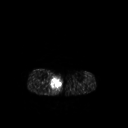
FDG PET of an extremity soft-tissue mass (from a PET/CT study), one axial slice; slice 129 of 267 in the series (ordered by position); 3.27 mm slice thickness; 128 × 128 image matrix, field of view 500 × 500 mm. Patient: male, 69 years. Case-level facts recorded for this patient, not image findings: histological type: pleiomorphic liposarcoma; grade: high; site of the primary tumour: right calf.
Outlined on this slice (expert contour drawn on MRI and transferred to this co-registered scan by the dataset authors):
- gross tumour volume including surrounding oedema: bounding box (x1, y1, x2, y2) in pixels: (50, 75, 62, 94)
- gross tumour volume (mass): (50, 77, 62, 89)